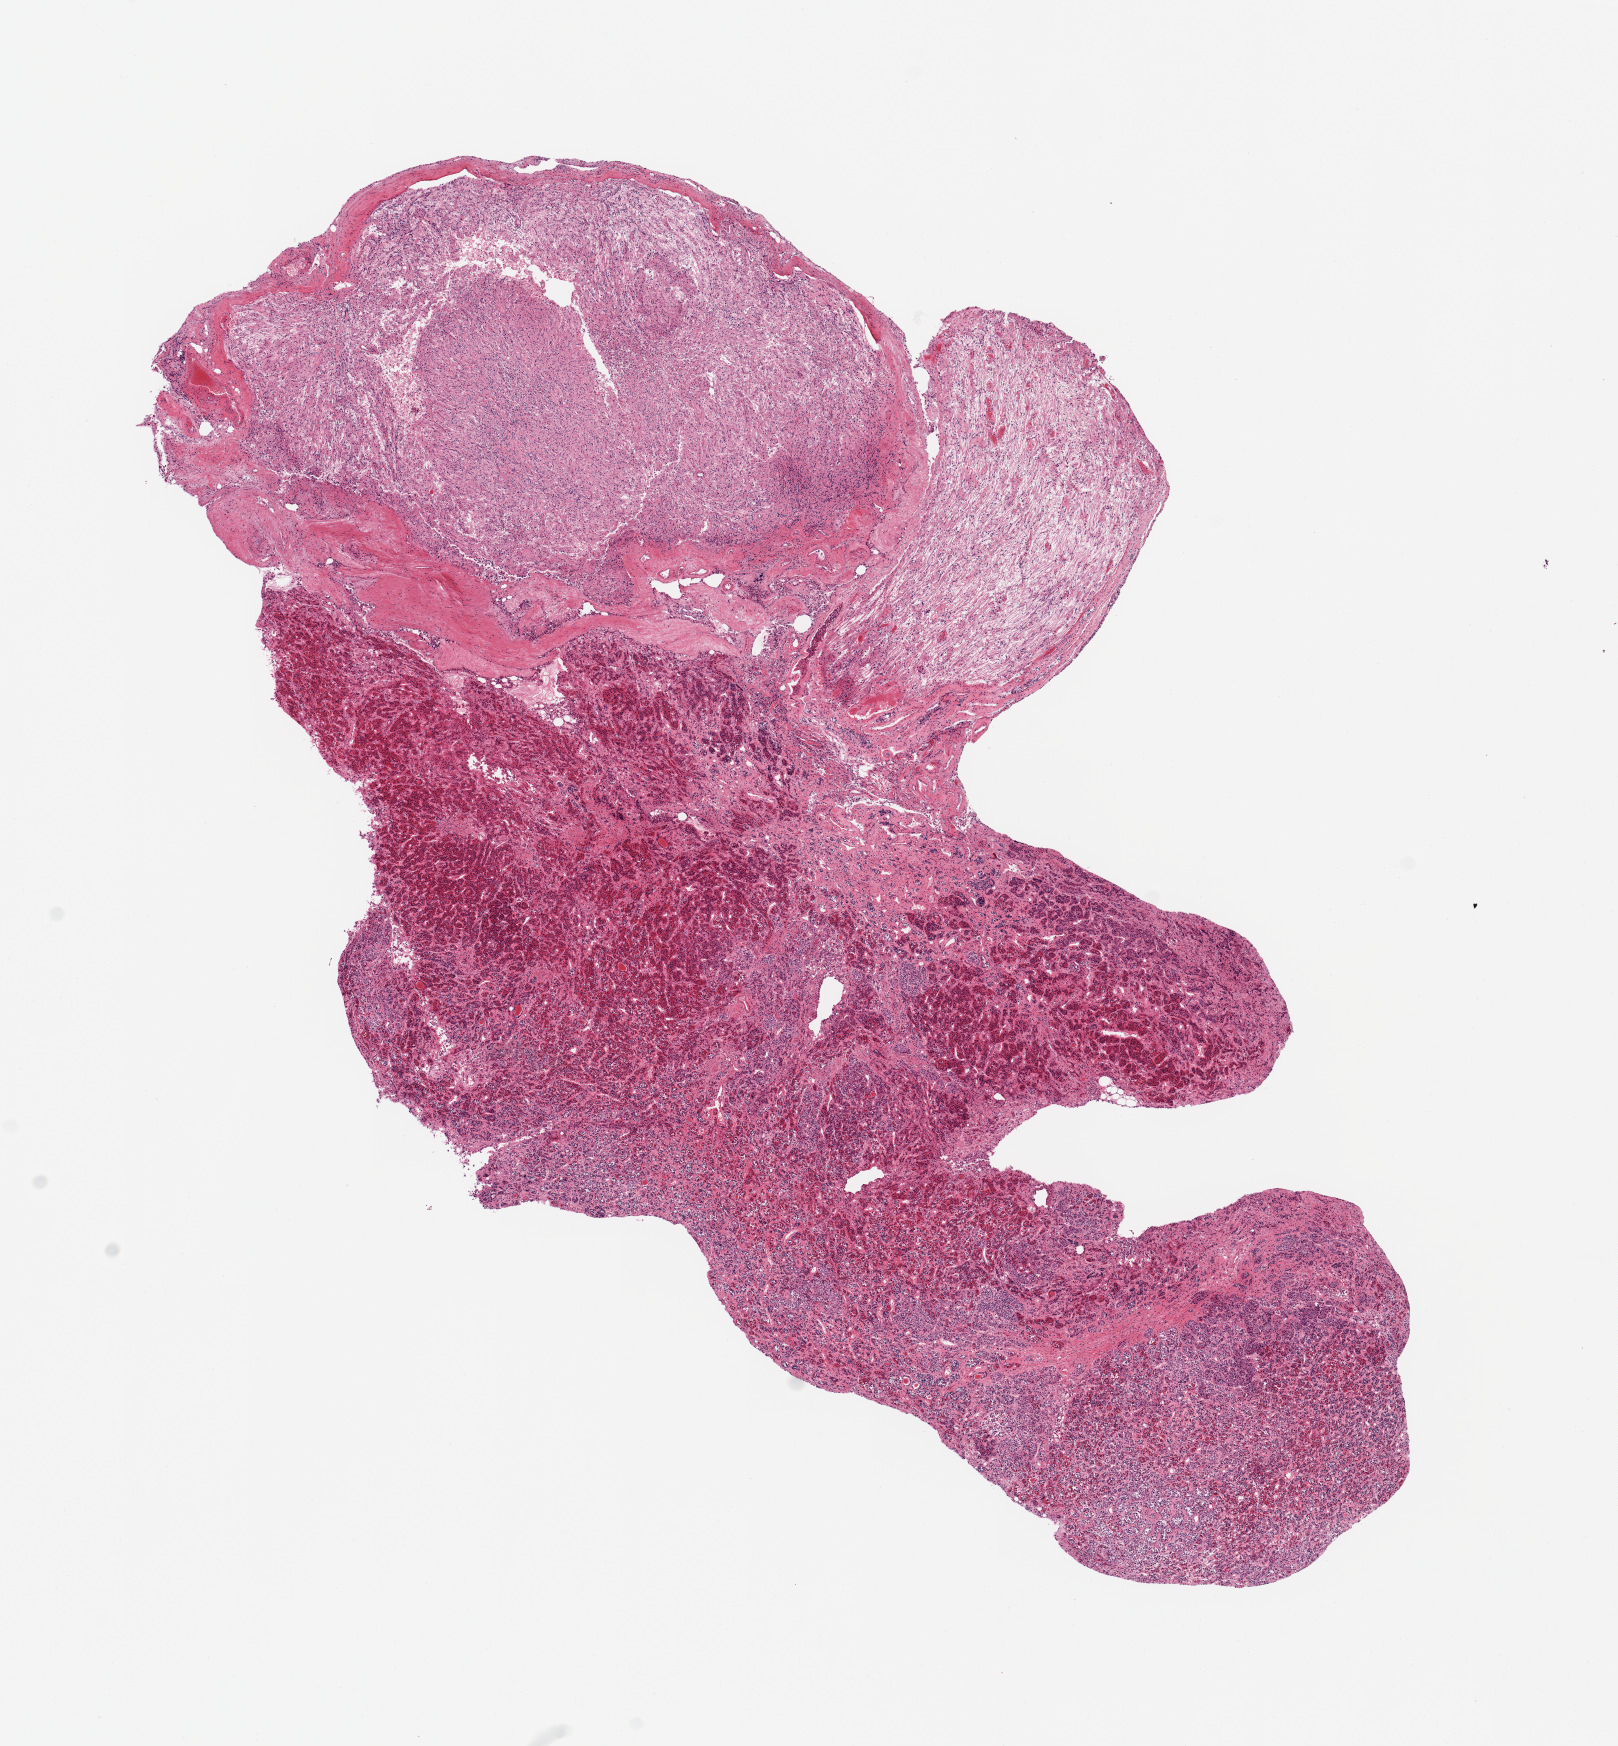
Digitized H&E-stained section, shown as a low-resolution overview of the whole scanned area (about 12.8 x 13.8 mm); PAXgene-fixed, paraffin-embedded tissue; sampled site (target tissue): pituitary; donor tissue sample. Donor: female.
• review note (as recorded): 1 piece; anterior and posterior lobes about equal [posterior]